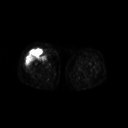
FDG PET of an extremity soft-tissue mass (from a PET/CT study), one axial slice; slice 231 of 311 in the series (ordered by position); 3.27 mm slice thickness; 128 × 128 image matrix. Patient: female, 57 years. From the clinical record (not read from this slice): histological type: pleiomorphic undifferentiated sarcoma; grade: high; site of the primary tumour: right quadricep.
Annotated regions visible in this slice (expert contour drawn on MRI and transferred to this co-registered scan by the dataset authors):
- tumour plus oedema (research contour): bounding box [x1, y1, x2, y2] px = [25, 50, 46, 70]
- tumour (research contour): [28, 50, 45, 57]